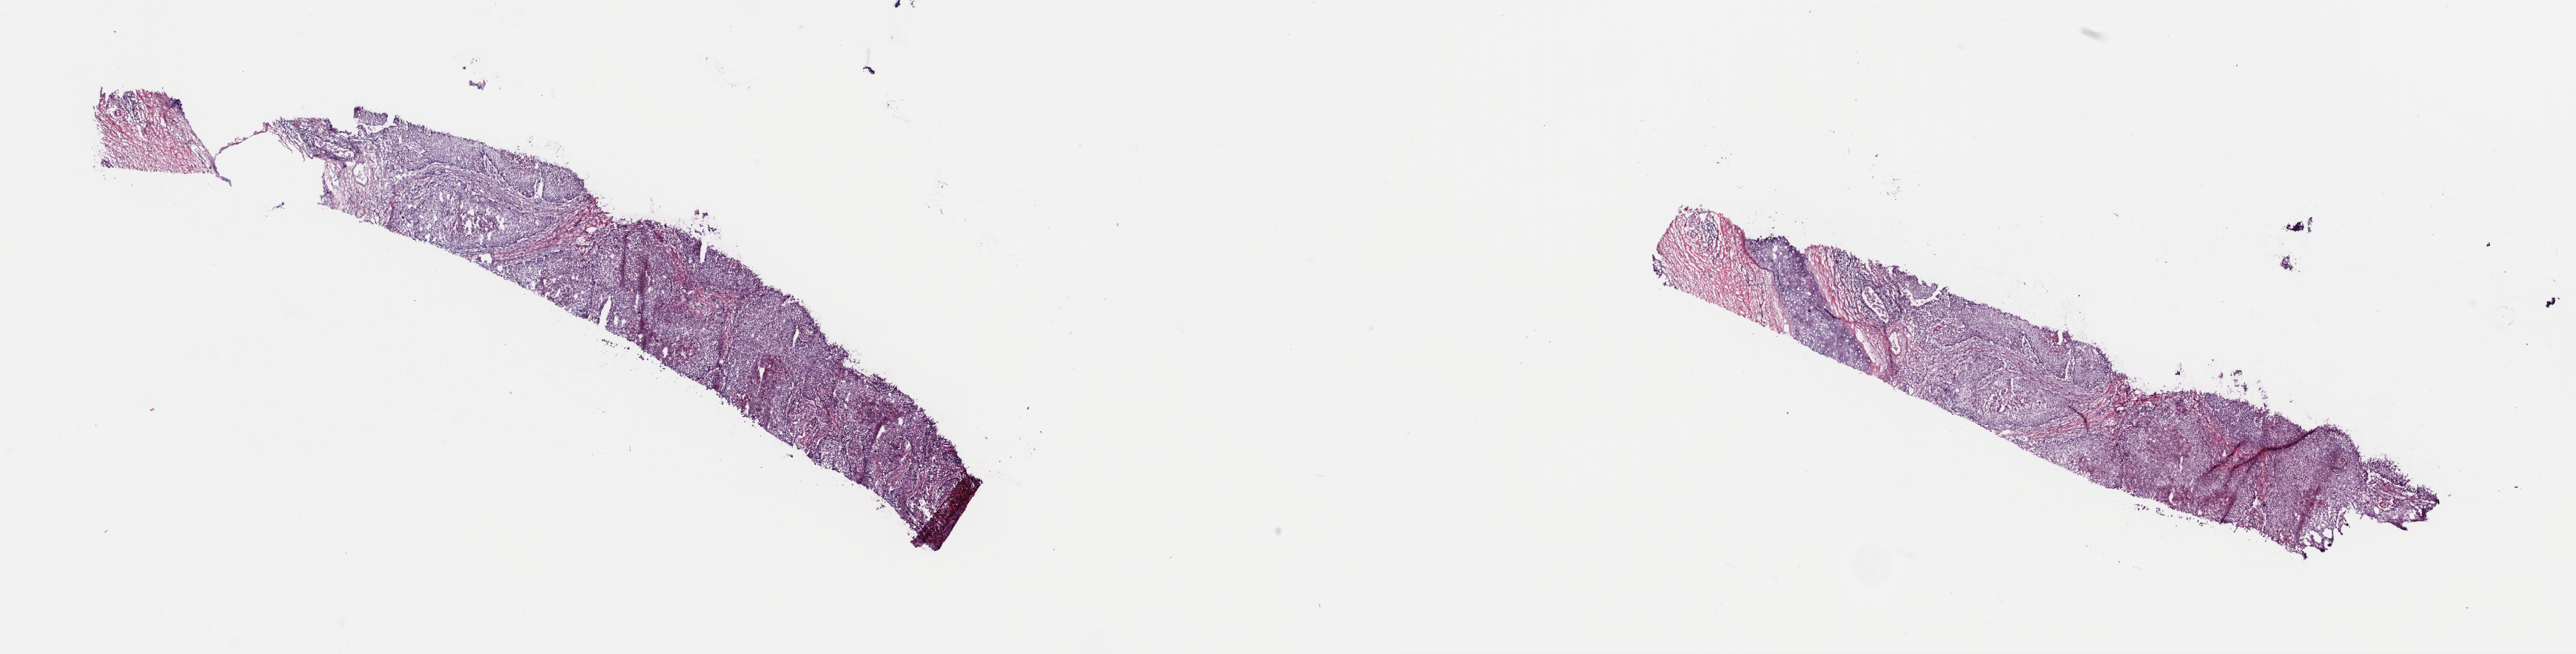
Digitized H&E-stained tissue section (whole slide), low-resolution overview of the scanned area, about 27.5 x 7.0 mm; frozen section; primary tumour sample from the lung. Male, age 84 years at initial diagnosis. Pathologist review of this section (percent, as recorded): tumour cells 90%, tumour nuclei 85%, normal cells 0%, stromal cells 5%, necrosis 5%. Inflammatory infiltration, as recorded: lymphocyte infiltration 0%, monocyte infiltration 0%, neutrophil infiltration 0%.
AJCC pathologic stage: IIA (7th edition). Histologic diagnosis: Squamous cell carcinoma, NOS (upper lobe, lung). Laterality: left.